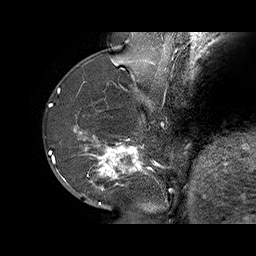
Breast MRI (dynamic contrast-enhanced), one sagittal slice; slice 21 of 70 in the series (ordered by position); dynamic contrast-enhanced series, time point 2 of 6 at this slice position (early post-contrast); 1.5 T; TE 4.5 ms, TR 32.4 ms; 3 mm slice thickness; 256 × 256 image matrix, field of view 180 × 180 mm. Female patient. From the clinical record (not read from this slice): setting: breast cancer imaged before/during neoadjuvant chemotherapy; receptor status: HR-positive, HER2-negative.
Structures marked on this image (semi-automatically segmented with operator editing):
- analysis volume of interest (the breast-tissue region the enhancement analysis was run in; not a lesion): bounding box [x1, y1, x2, y2] px = [71, 128, 159, 202]
- tumour enhancement mask (voxels above the 100 % enhancement threshold inside the analysis volume of interest): [73, 128, 148, 190]